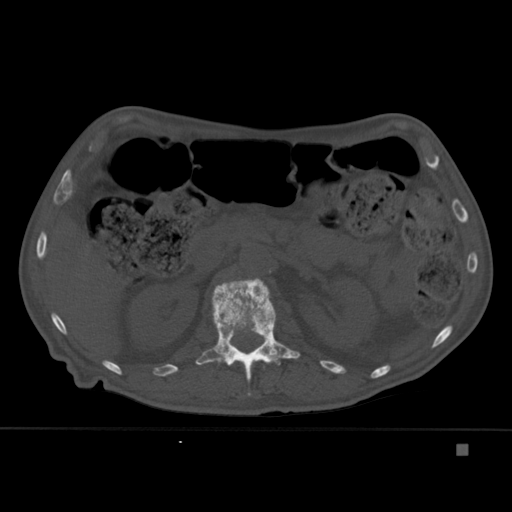
CT including the spine, one axial slice. Slice 182 of 451 in the series (ordered by position). Bone window (W 1800 / L 400 HU). 1.5 mm slice thickness. 512 × 512 image matrix, field of view 378 × 378 mm. Male patient, age 75 years. From the clinical record (not read from this slice): primary cancer: prostate.
Outlined on this slice (semi-automatic segmentation, software-assisted and operator-edited):
- L1 vertebra: bounding box <195,278,300,396> (left, top, right, bottom; pixels)
- T12 vertebra: <233,363,265,368>